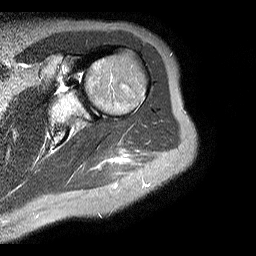
MRI of an extremity soft-tissue mass, one axial slice; position 15 of 20 along the scan axis; STIR; 4 mm slice thickness; 256 × 256 image matrix. Female patient. Case-level facts recorded for this patient, not image findings: histological type: malignant fibrous histiocytoma; grade: low; site of the primary tumour: left arm.
Outlined on this slice (expert manual segmentation):
- gross tumour volume (mass): bounding box <114,153,127,164> (left, top, right, bottom; pixels)